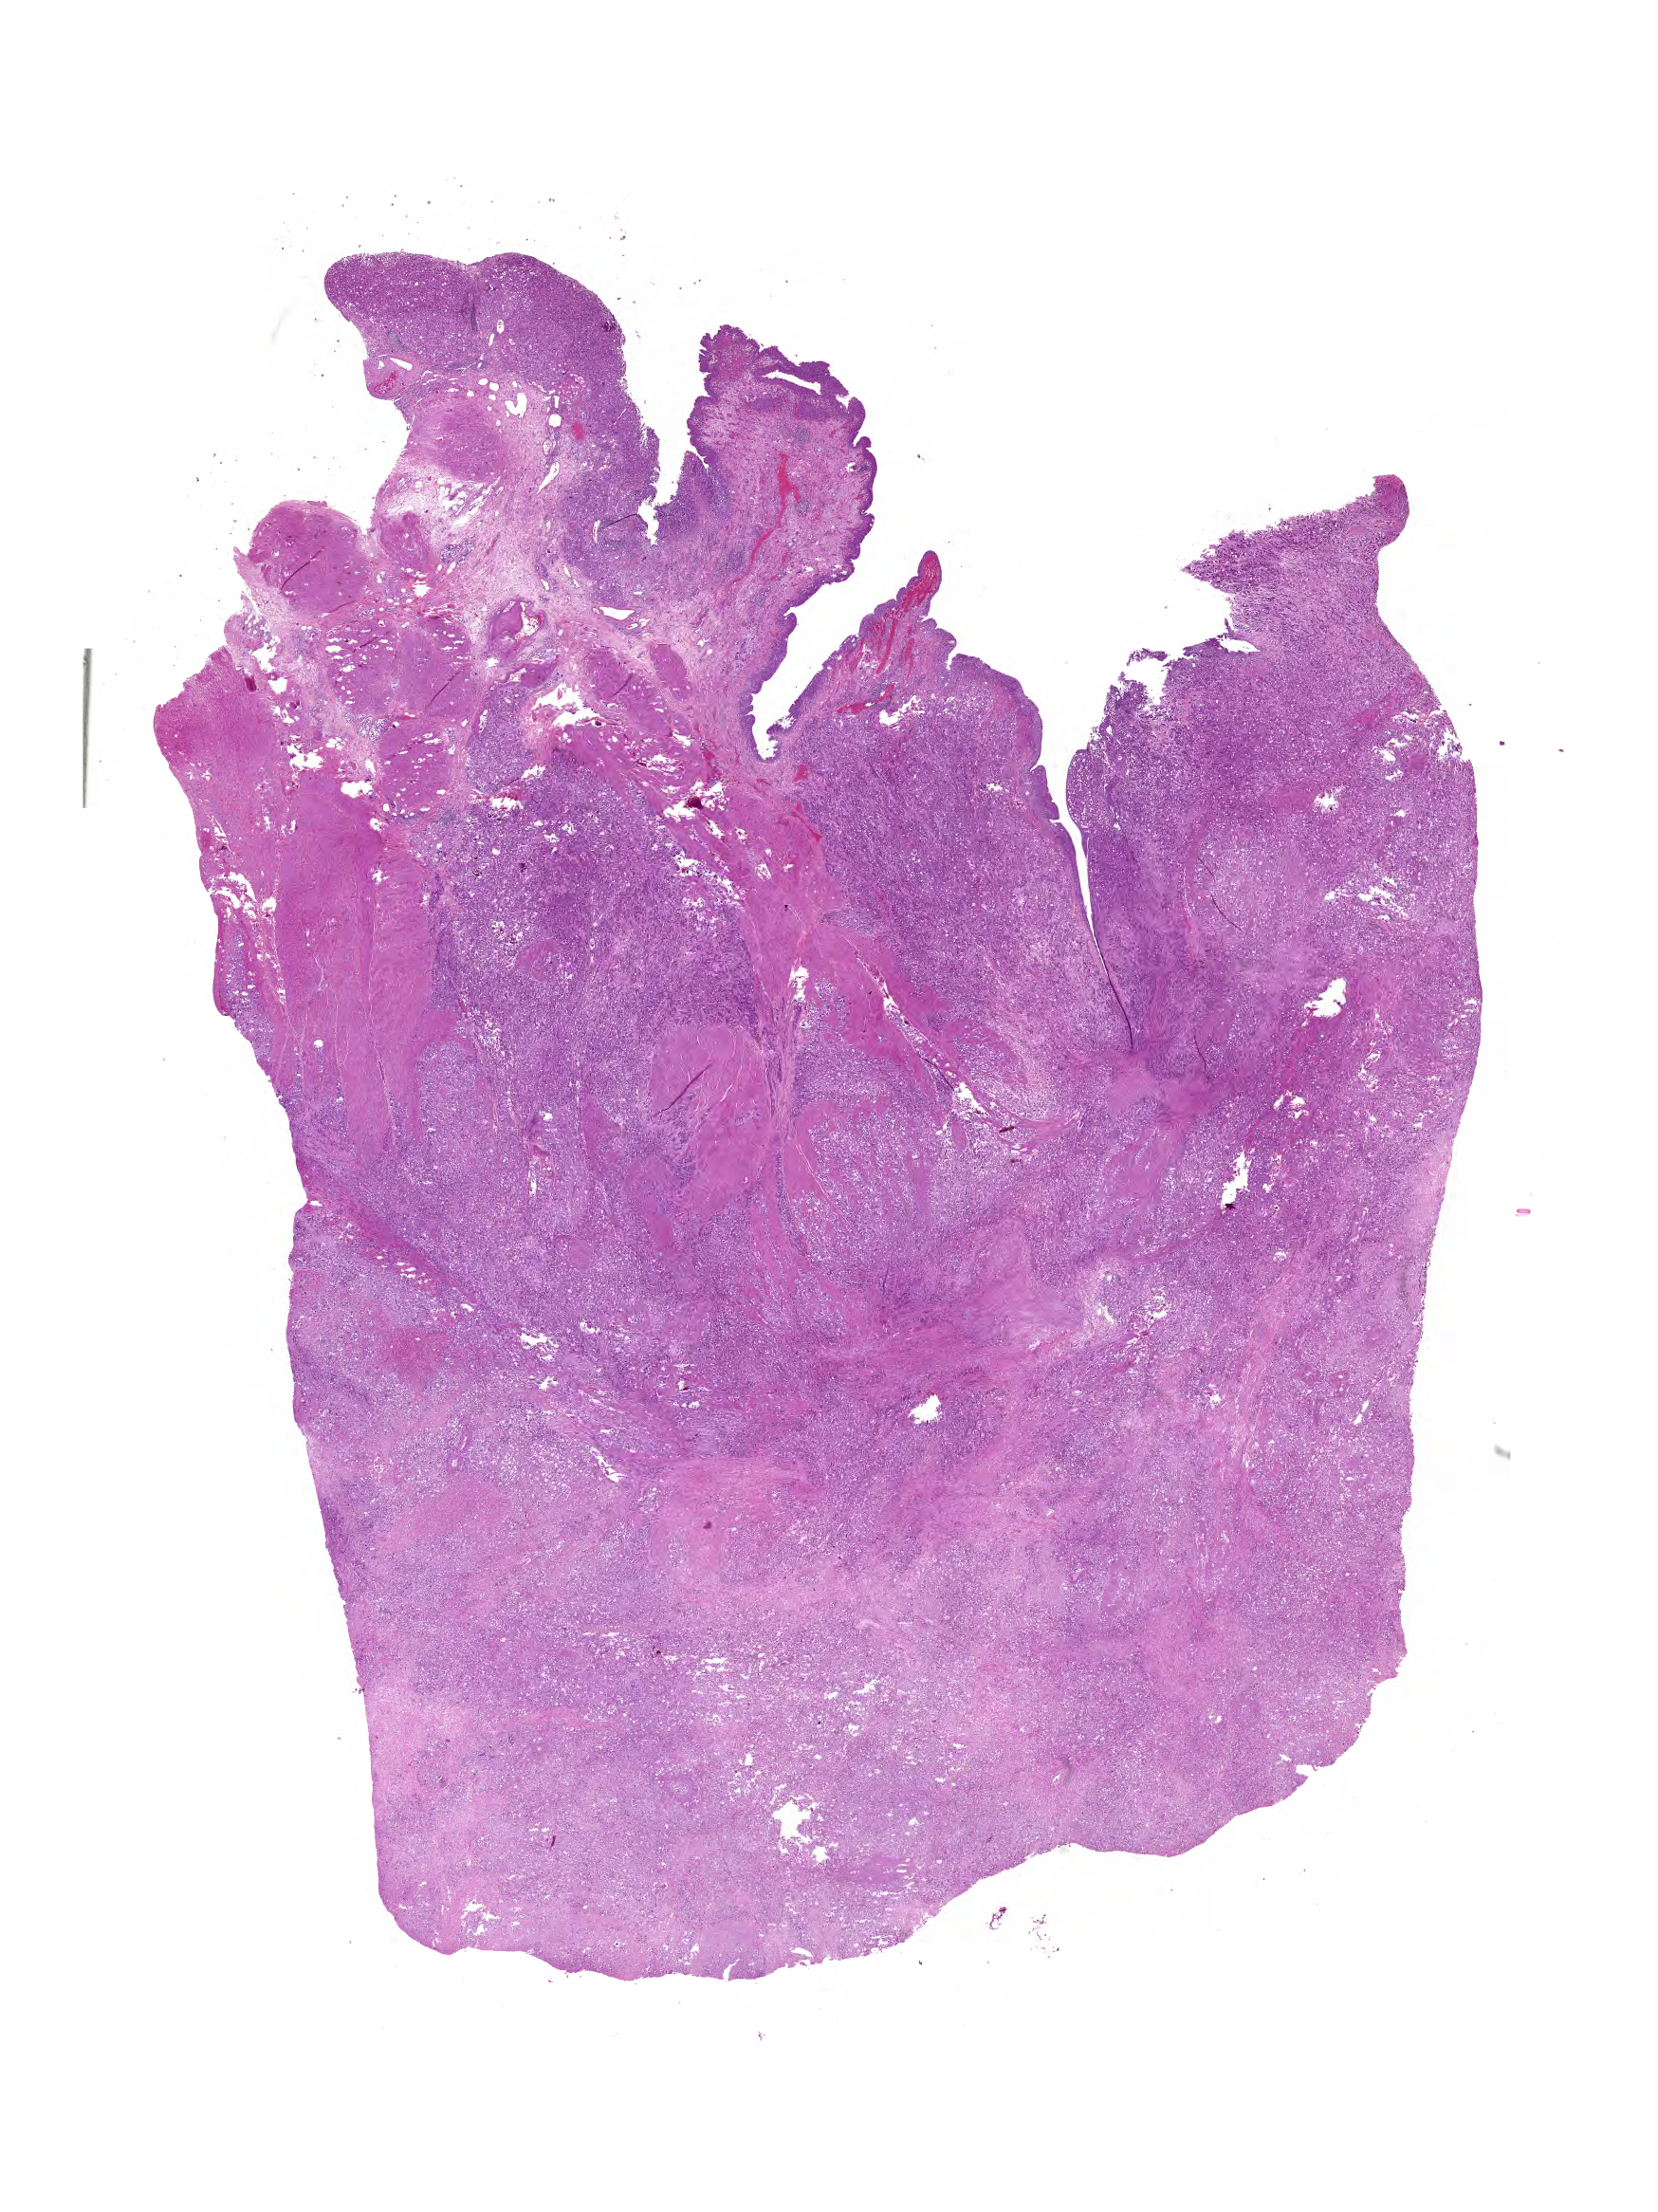
Hematoxylin and eosin (H&E) stained whole-slide image — low-resolution overview of the scanned area, about 21.8 x 29.0 mm (slide scanned at 40x), formalin-fixed paraffin-embedded (FFPE) diagnostic section, sample: primary tumour, bladder. Patient: female, age at initial diagnosis 76 years. Histologic grade: high grade.
* AJCC pathologic stage: III (7th edition)
* TNM: T4 NX MX
* diagnosis: Transitional cell carcinoma